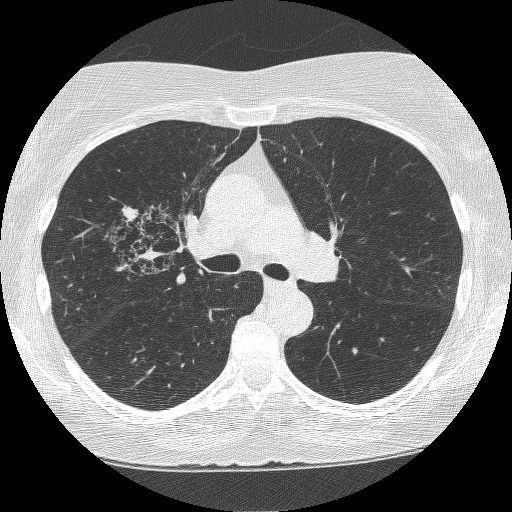
Axial slice from a low-dose chest CT screening exam. Second annual screen. Lung window (W 1500 / L -600 HU). 1.25 mm slice thickness. 120 kVp. Slice 154 of 249 in the series. 512 × 512 image matrix. Female participant, aged 64 years at enrolment. Former smoker at enrolment.
Expert-annotated lung lesion, bounding box [x1, y1, x2, y2] px = [115, 205, 206, 291]. The screening reader recorded 4 non-calcified nodules or masses ≥4 mm on this exam (right upper lobe, right upper lobe, right upper lobe, left upper lobe); which of them this box marks is not recorded. Later outcome: lung cancer diagnosed 381 days after this screen (after the third annual screen) — adenocarcinoma, NOS, right upper lobe, right middle lobe, right hilum, stage IV (AJCC 6th edition), 85 mm at pathology.